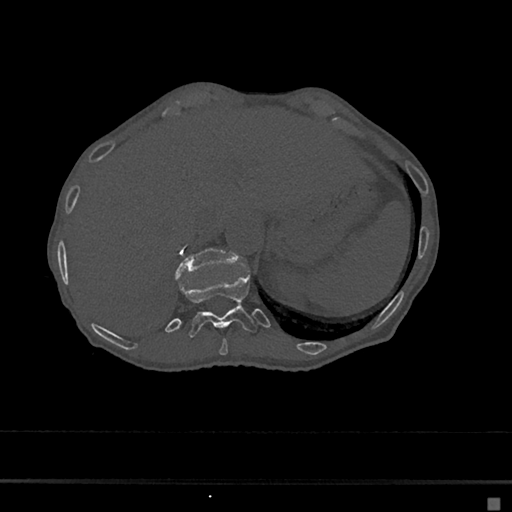
CT including the spine, one axial slice. Position 172 of 797 along the scan axis. Reconstruction kernel Br40s/3. Bone window (W 1800 / L 400 HU). 512 × 512 image matrix, field of view 360 × 360 mm. Patient: female, 68 years. Case-level facts recorded for this patient, not image findings: primary cancer: renal.
Outlined on this slice (semi-automatically segmented with operator editing):
- T10 vertebra: bounding box (x1, y1, x2, y2) in pixels: (219, 338, 228, 356)
- T11 vertebra: (176, 275, 257, 338)
- T12 vertebra: (175, 247, 237, 278)